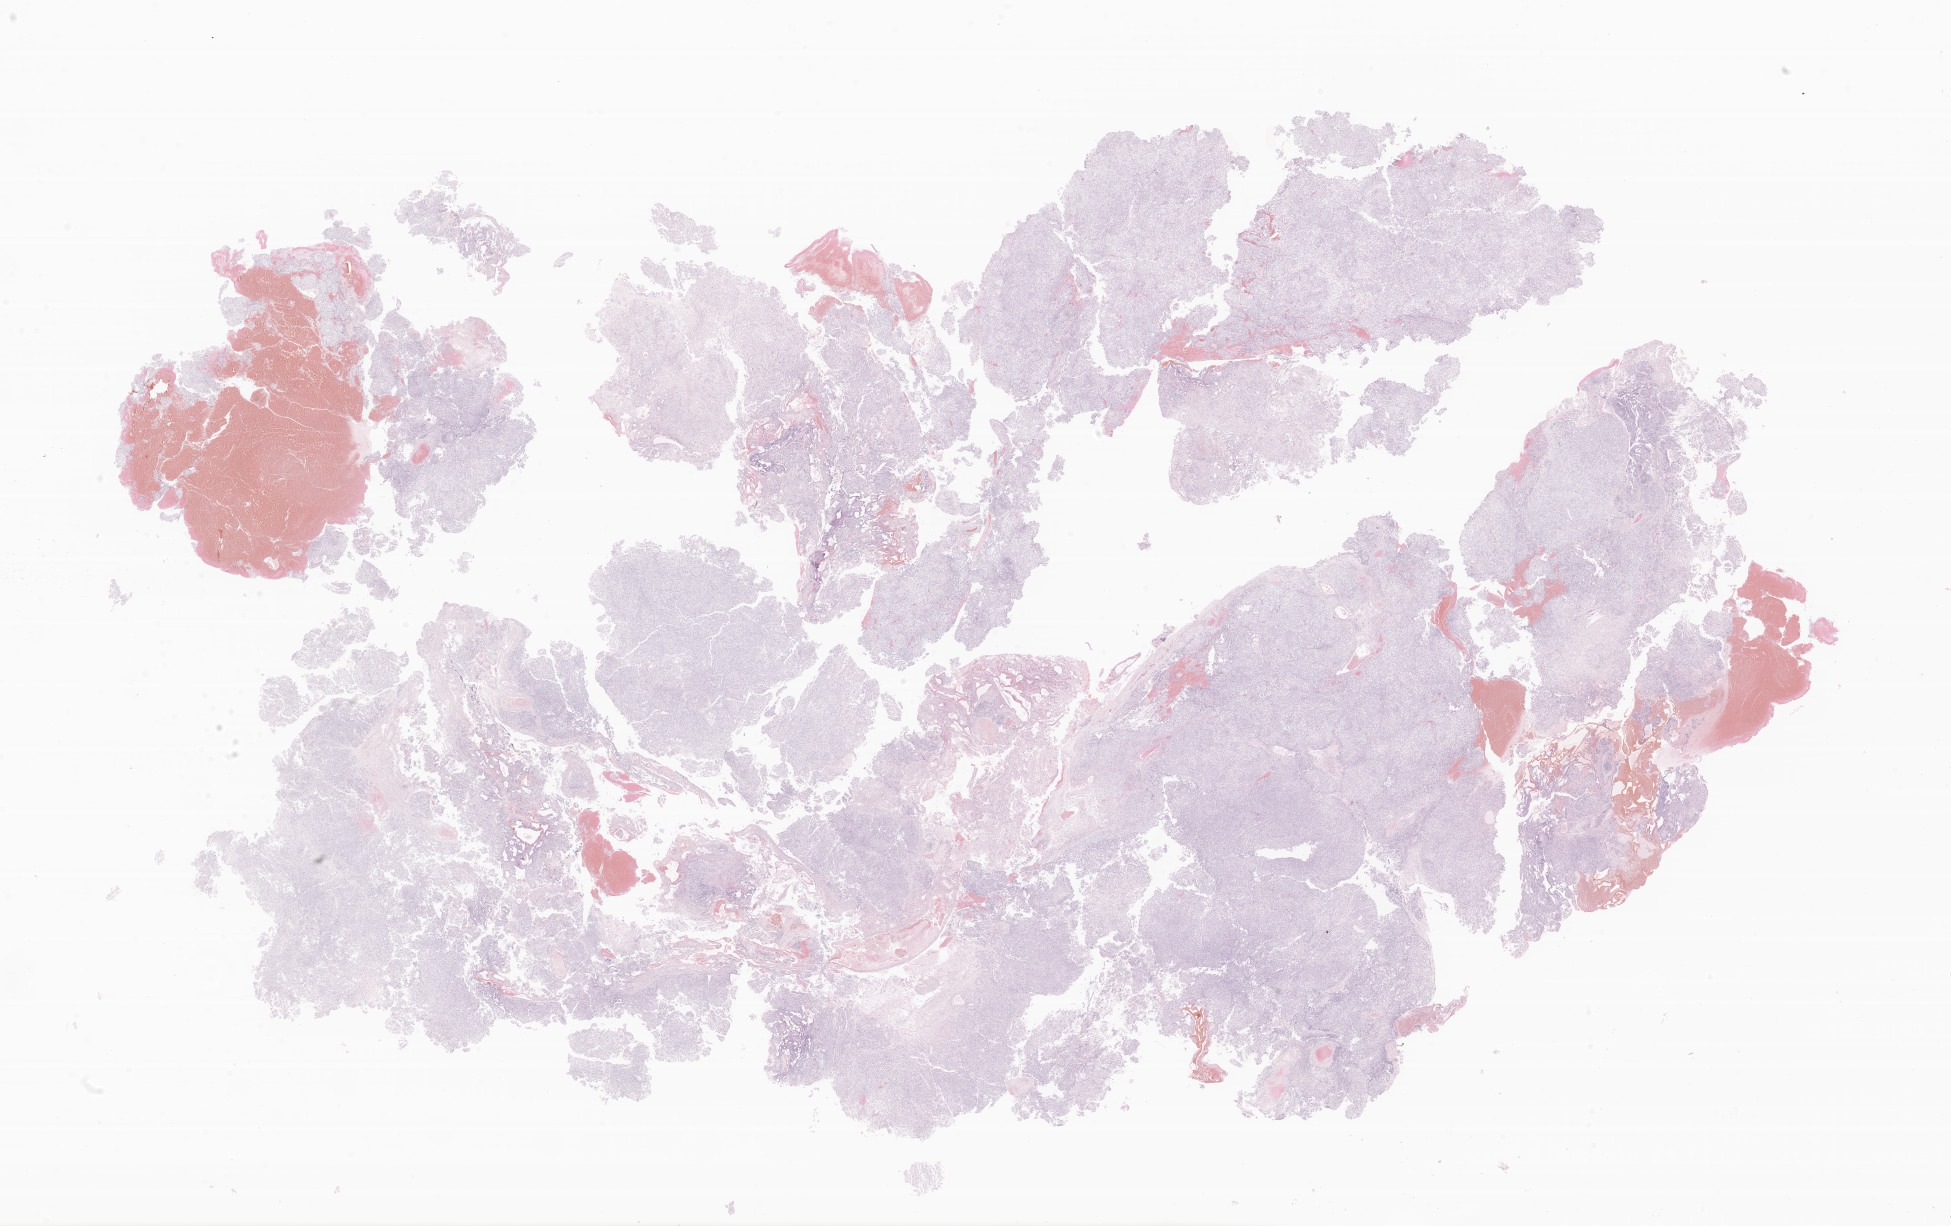
Haematoxylin and eosin whole-slide image of tumor tissue from the brain, a low-resolution overview of the entire scanned area, about 32.9 x 20.7 mm. Formalin-fixed, paraffin-embedded (FFPE) tissue. Patient: female, age 811 days (about 2.2 years).
Diagnosis (ICD-O-3 morphology term): Atypical teratoid/rhabdoid tumor.